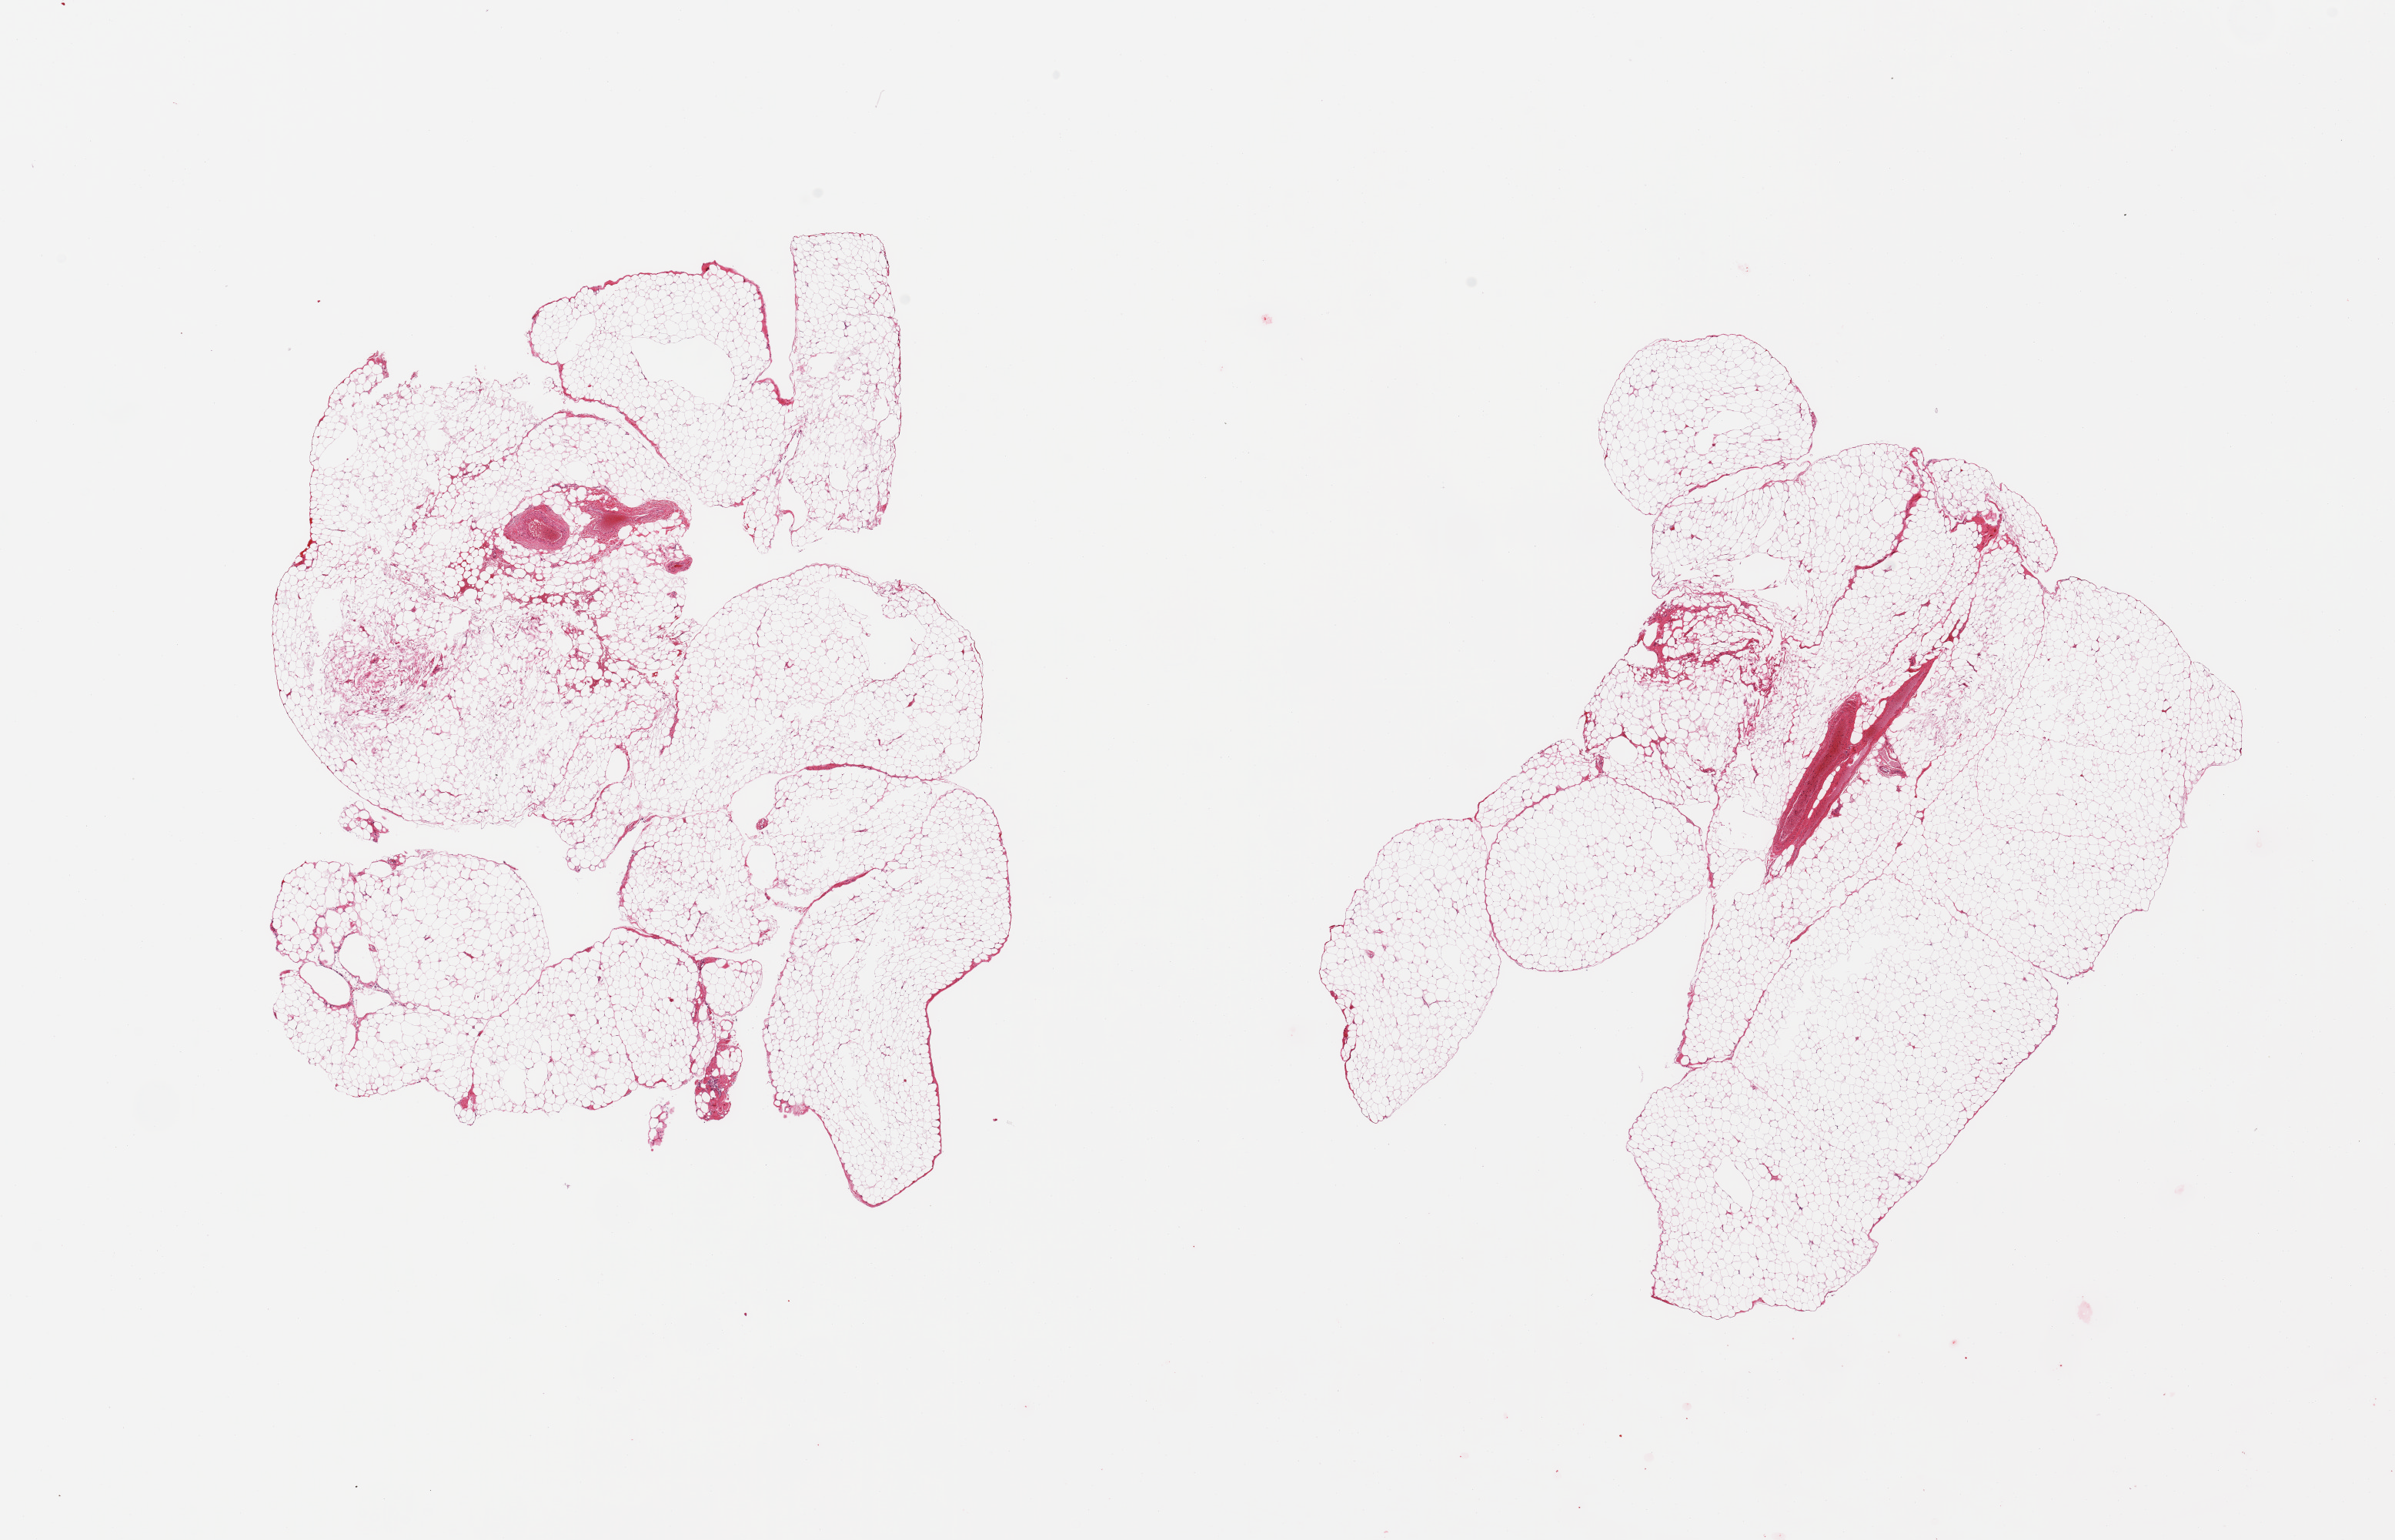
Digitized H&E-stained section — a low-resolution overview of the entire scanned area, about 24.6 x 15.8 mm, PAXgene-fixed paraffin-embedded (PFPE) section, section of omentum (target tissue), donor tissue sample. Donor sex: male.
* review note (as recorded): 2 pieces; mature fat, few larger vessels